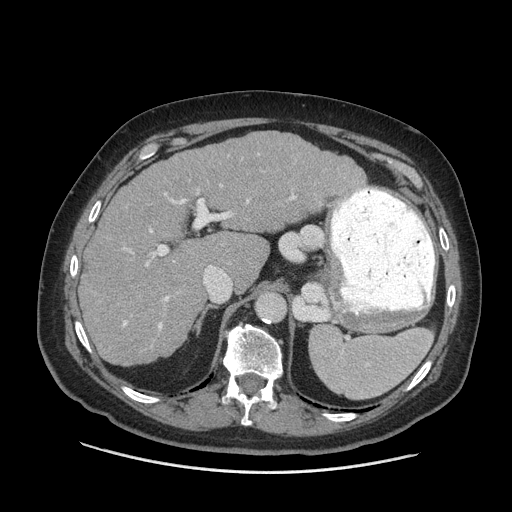
Contrast-enhanced abdominal CT (liver protocol), one axial slice. Position 44 of 77 along the scan axis. 140 kVp. Soft-tissue window (W 400 / L 40 HU). 512 × 512 image matrix. From the clinical record (not read from this slice): diagnosis: hepatocellular carcinoma (patient treated with transarterial chemoembolisation; whether this scan precedes or follows treatment is not stated here); TNM stage (as recorded): Stage-I; Child-Pugh class: A; tumour differentiation: well differentiated; tumour size: 3.8 cm.
Annotated regions visible in this slice (semi-automatically segmented with operator editing):
- liver parenchyma outside the tumour (the mass and vessels are separate outlines, so this box may not span the whole liver): bounding box <79,132,364,366> (left, top, right, bottom; pixels)
- liver vessels: <123,185,296,330>